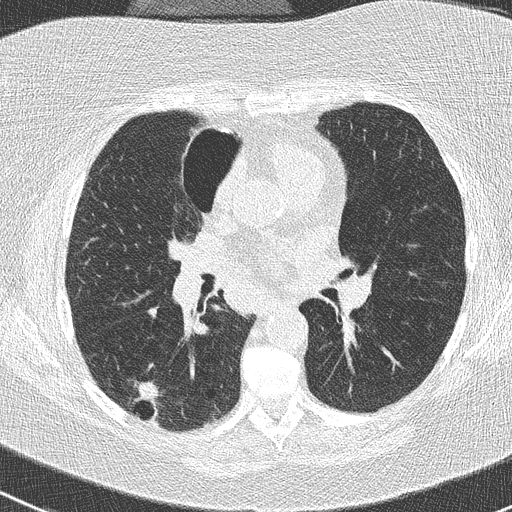
Low-dose screening chest CT, one axial slice; position 141 of 261 along the scan axis; lung window (W 1500 / L -600 HU); 2 mm slice thickness; 512 × 512 image matrix, field of view 310 × 310 mm.
Outlined on this slice (manually delineated by an expert):
- lesion 1 (tumor, lower lobe of right lung): bounding box <134,381,159,403> (left, top, right, bottom; pixels)